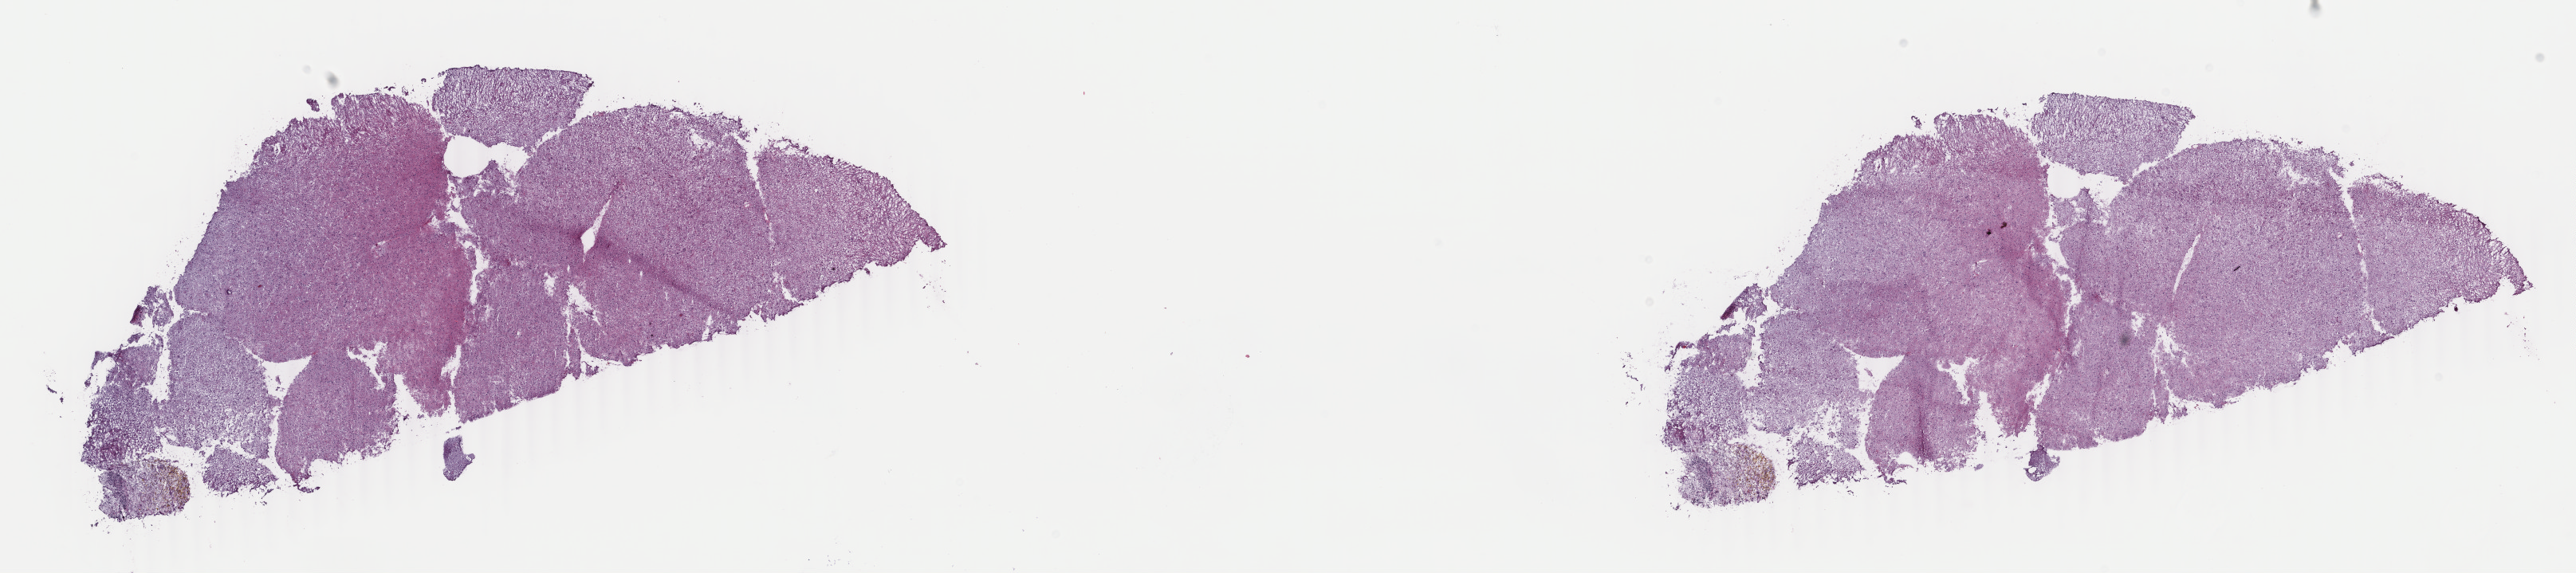
Whole-slide histology image, H&E, whole scanned area (about 25.7 x 5.7 mm) shown as a low-resolution overview, frozen section from the top of the tissue portion, sample: primary tumour, brain. Male patient; age at initial diagnosis 47 years. Histologic grade: G2 (moderately differentiated). Composition of this section per pathologist review: tumour cells 50%, tumour nuclei 75%, normal cells 10%, stromal cells 40%, necrosis 0%. Infiltration values recorded for this section: lymphocyte infiltration 5%, monocyte infiltration 0%, neutrophil infiltration 0%.
Laterality: right. Histologic diagnosis: Oligodendroglioma, NOS (cerebrum).